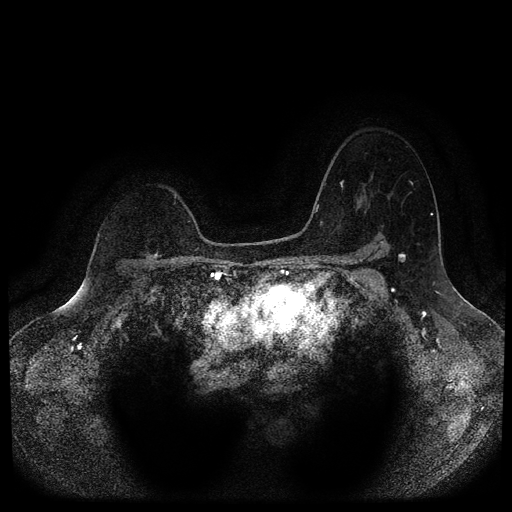
Breast MRI (dynamic contrast-enhanced, multi-phase), one axial slice; position 77 of 116 along the scan axis; dynamic contrast-enhanced series, time point 2 of 5 at this slice position (early post-contrast); 1.5 T; TE 2.6 ms, TR 5.4 ms; 2 mm slice thickness; 512 × 512 image matrix. Female patient, age 64 years.
Outlined on this slice (semi-automatically segmented with operator editing):
- breast lesion (labelled benign in the annotation): box from (x=144, y=239) to (x=160, y=260) px